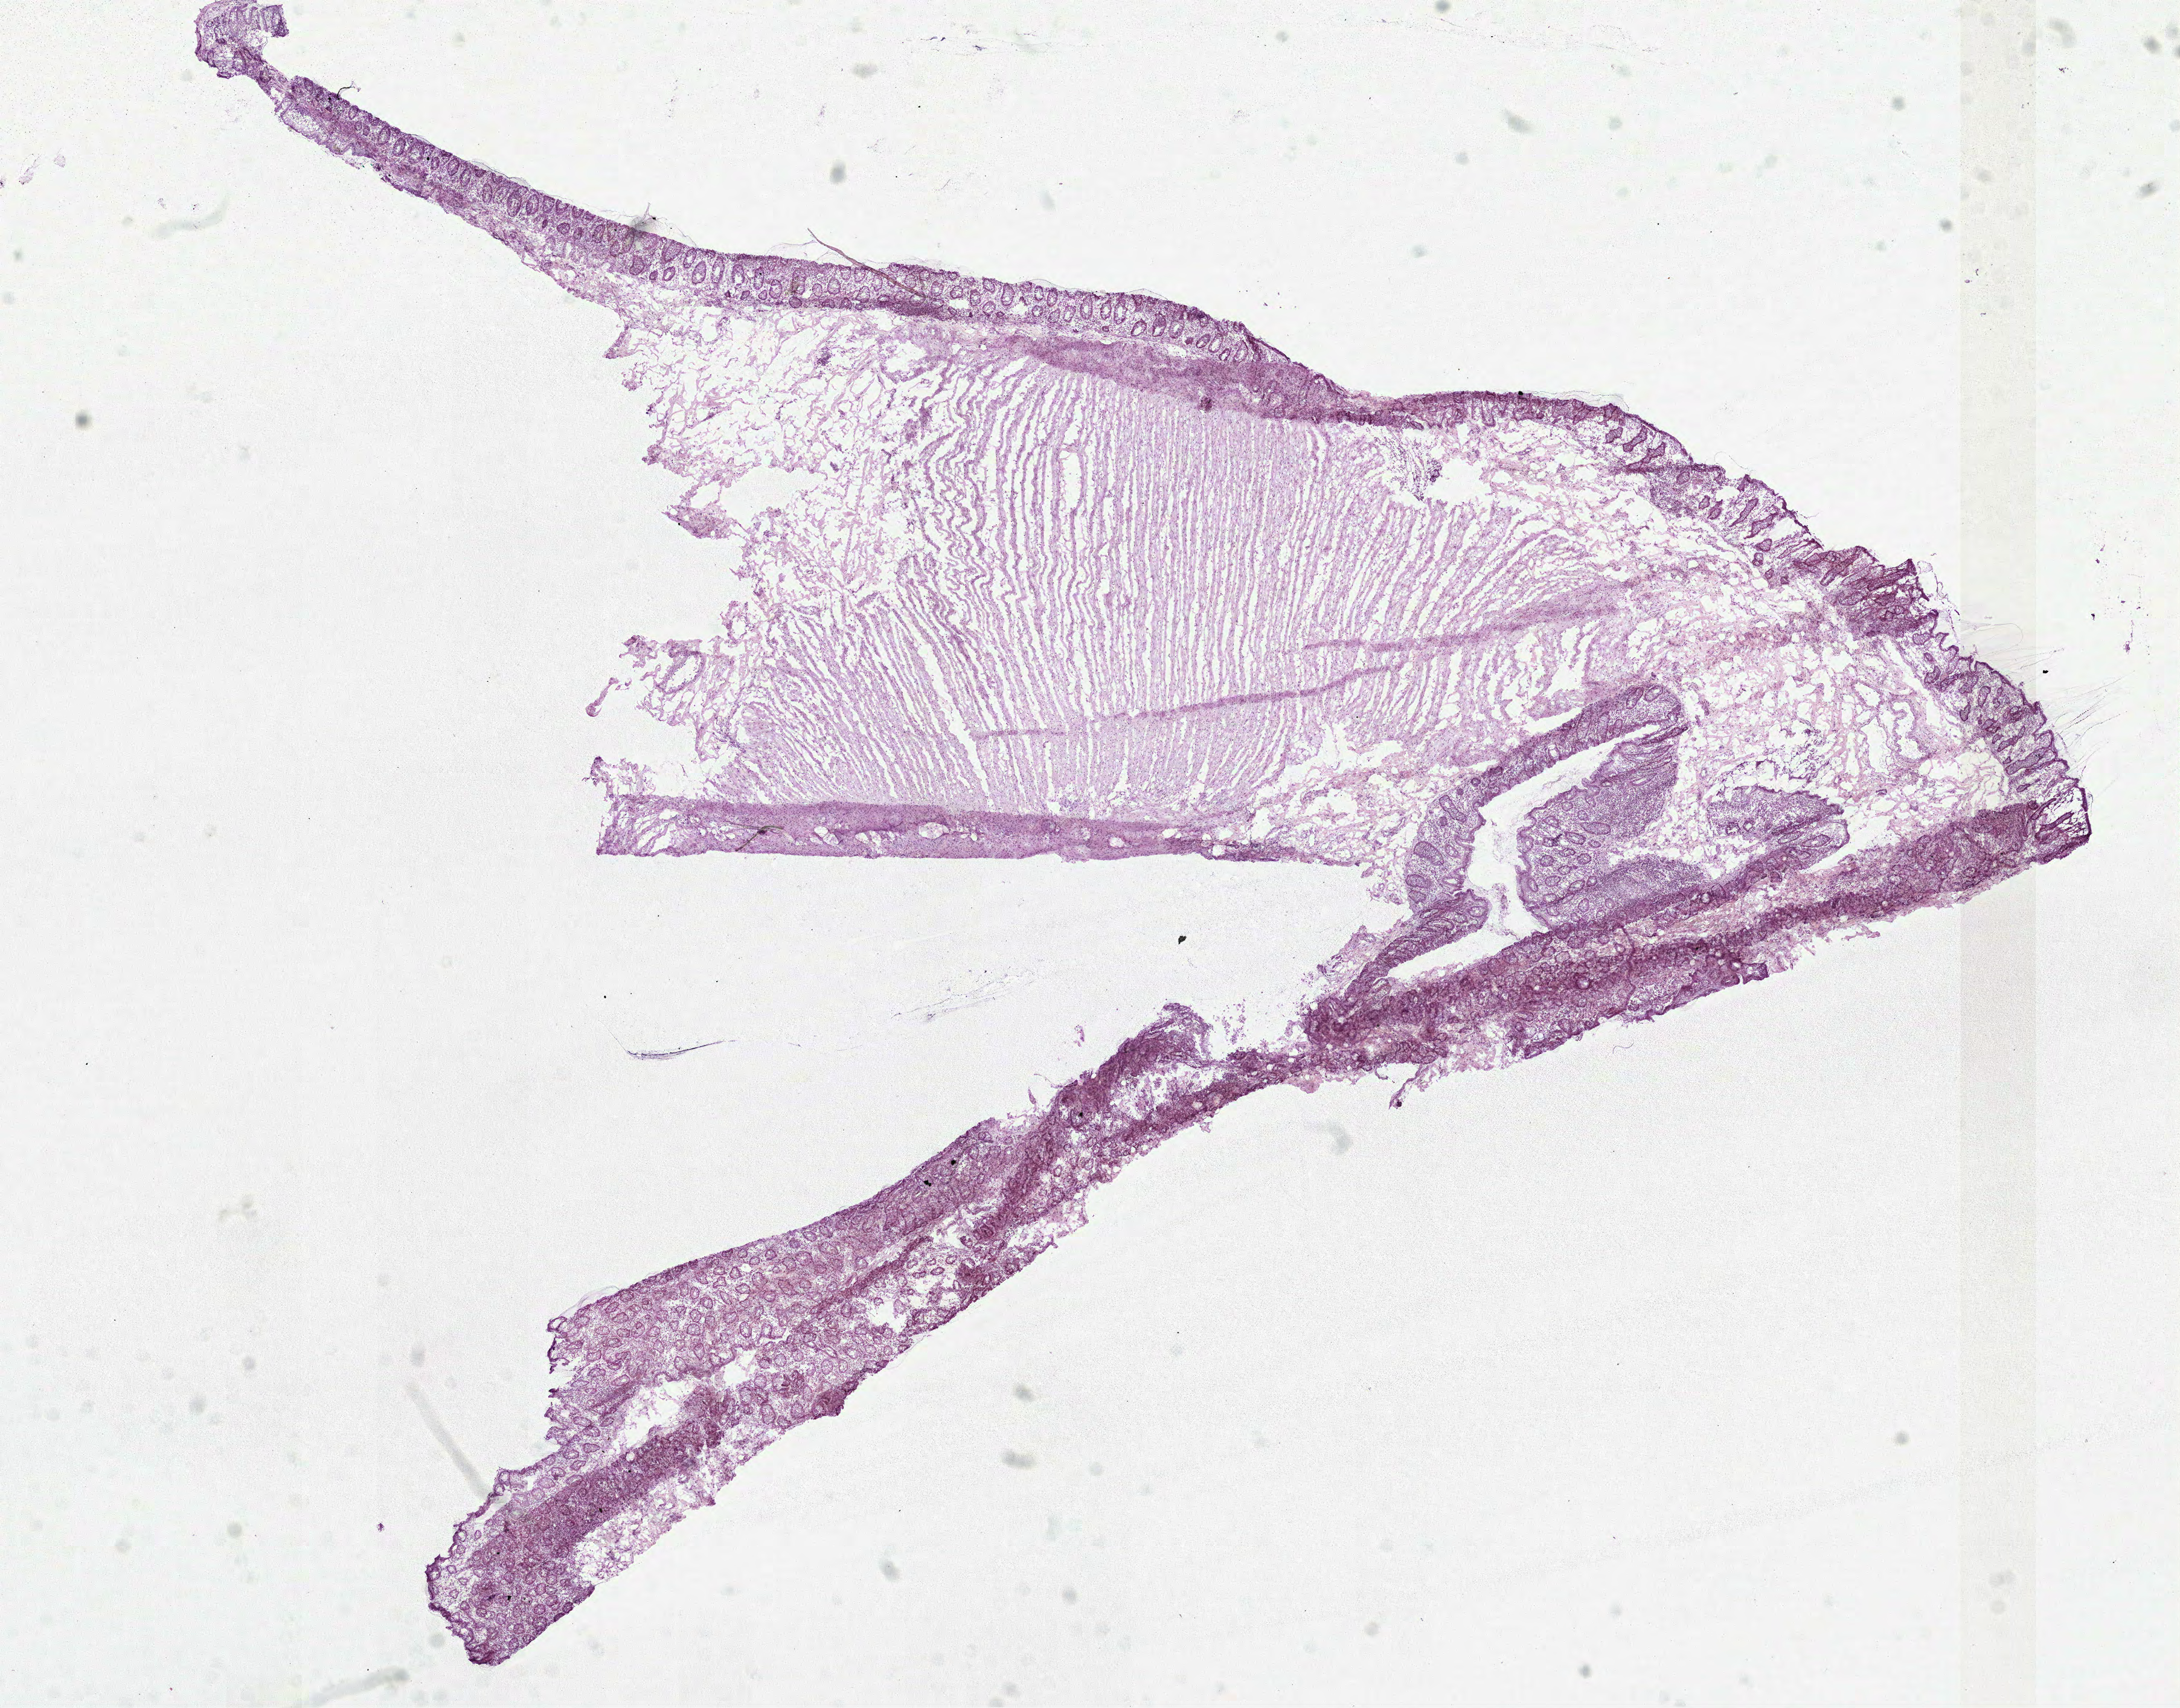
Hematoxylin and eosin (H&E) stained whole-slide image, a low-resolution overview of the entire scanned area, about 14.6 x 11.4 mm, frozen section from the top of the tissue portion, solid tissue normal (non-tumour tissue) sample from the colon. Female patient.
* this section: solid tissue normal sample (biorepository sample class)
* patient diagnosis: Mucinous adenocarcinoma